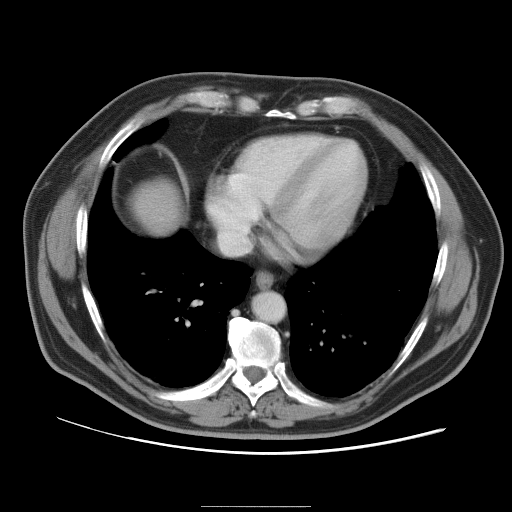
Contrast-enhanced abdominal CT, one axial slice. Intravenous contrast given. Soft-tissue window (W 400 / L 40 HU). 512 × 512 image matrix, field of view 399 × 399 mm. Male patient, age 64 years. Case-level facts recorded for this patient, not image findings: diagnosis: colorectal cancer liver metastases, imaged before liver resection.
Annotated regions visible in this slice (outlined manually by an expert reader):
- liver: box from (x=134, y=181) to (x=181, y=233) px
- planned liver remnant (the part of the liver to remain after resection): (x=133, y=182)–(x=180, y=234)